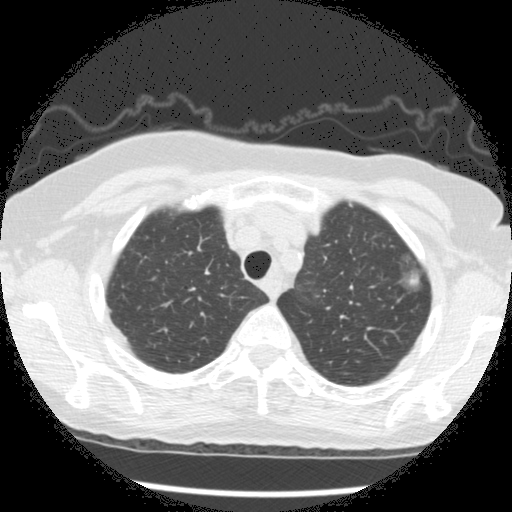
Low-dose screening chest CT, one axial slice; position 230 of 266 along the scan axis; 120 kVp; lung window (W 1500 / L -600 HU); 512 × 512 image matrix.
Structures marked on this image (expert manual segmentation):
- lesion 1 (tumor, upper lobe of left lung): bounding box [x1, y1, x2, y2] px = [407, 273, 419, 287]